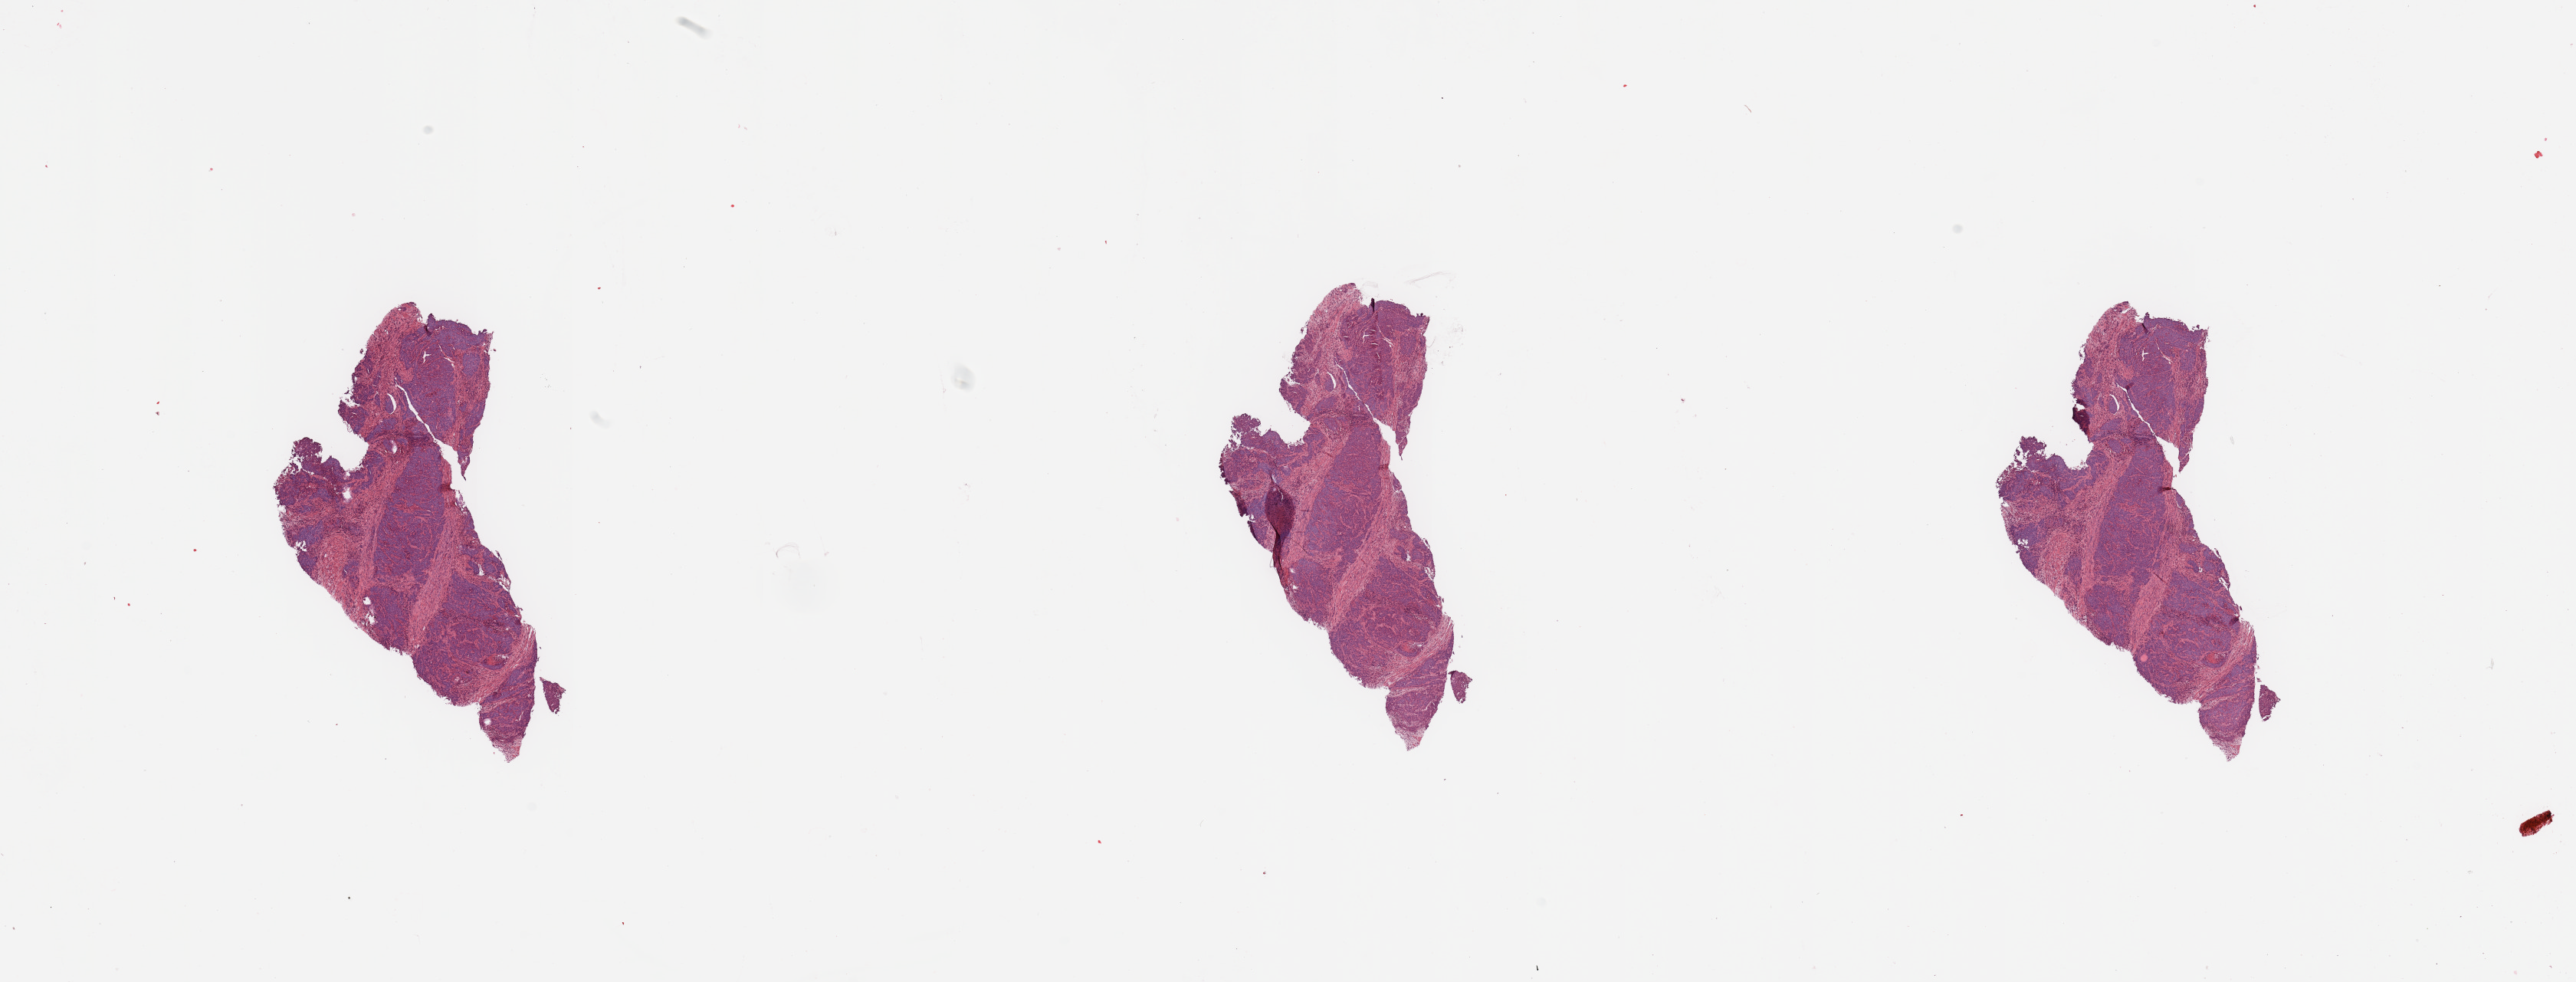
Whole-slide histology image, H&E — low-resolution overview of the scanned area, about 26.6 x 10.1 mm (acquisition: 20x scan), tumour tissue sample, sampled site: uterus. 63-year-old female patient. Histologic grade: G3 (poorly differentiated). Composition of this section per pathologist review: tumour nuclei 80%, necrosis 2%.
- diagnosis: Endometrioid adenocarcinoma, NOS
- AJCC pathologic stage: III
- primary tumour site (as recorded): anterior endometrium